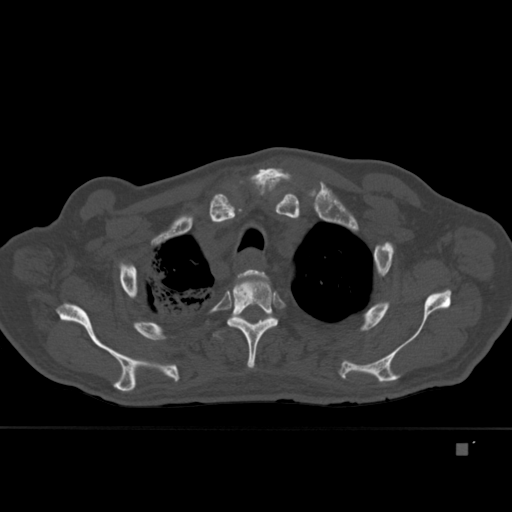
CT including the spine, one axial slice; position 334 of 451 along the scan axis; bone window (W 1800 / L 400 HU); 1.5 mm slice thickness; 512 × 512 image matrix. Male patient, age 75 years. Case-level facts recorded for this patient, not image findings: primary cancer: prostate.
Outlined on this slice (semi-automatic segmentation, software-assisted and operator-edited):
- T2 vertebra: bounding box <237,269,270,284> (left, top, right, bottom; pixels)
- T3 vertebra: <225,276,278,369>
- T4 vertebra: <213,318,265,339>